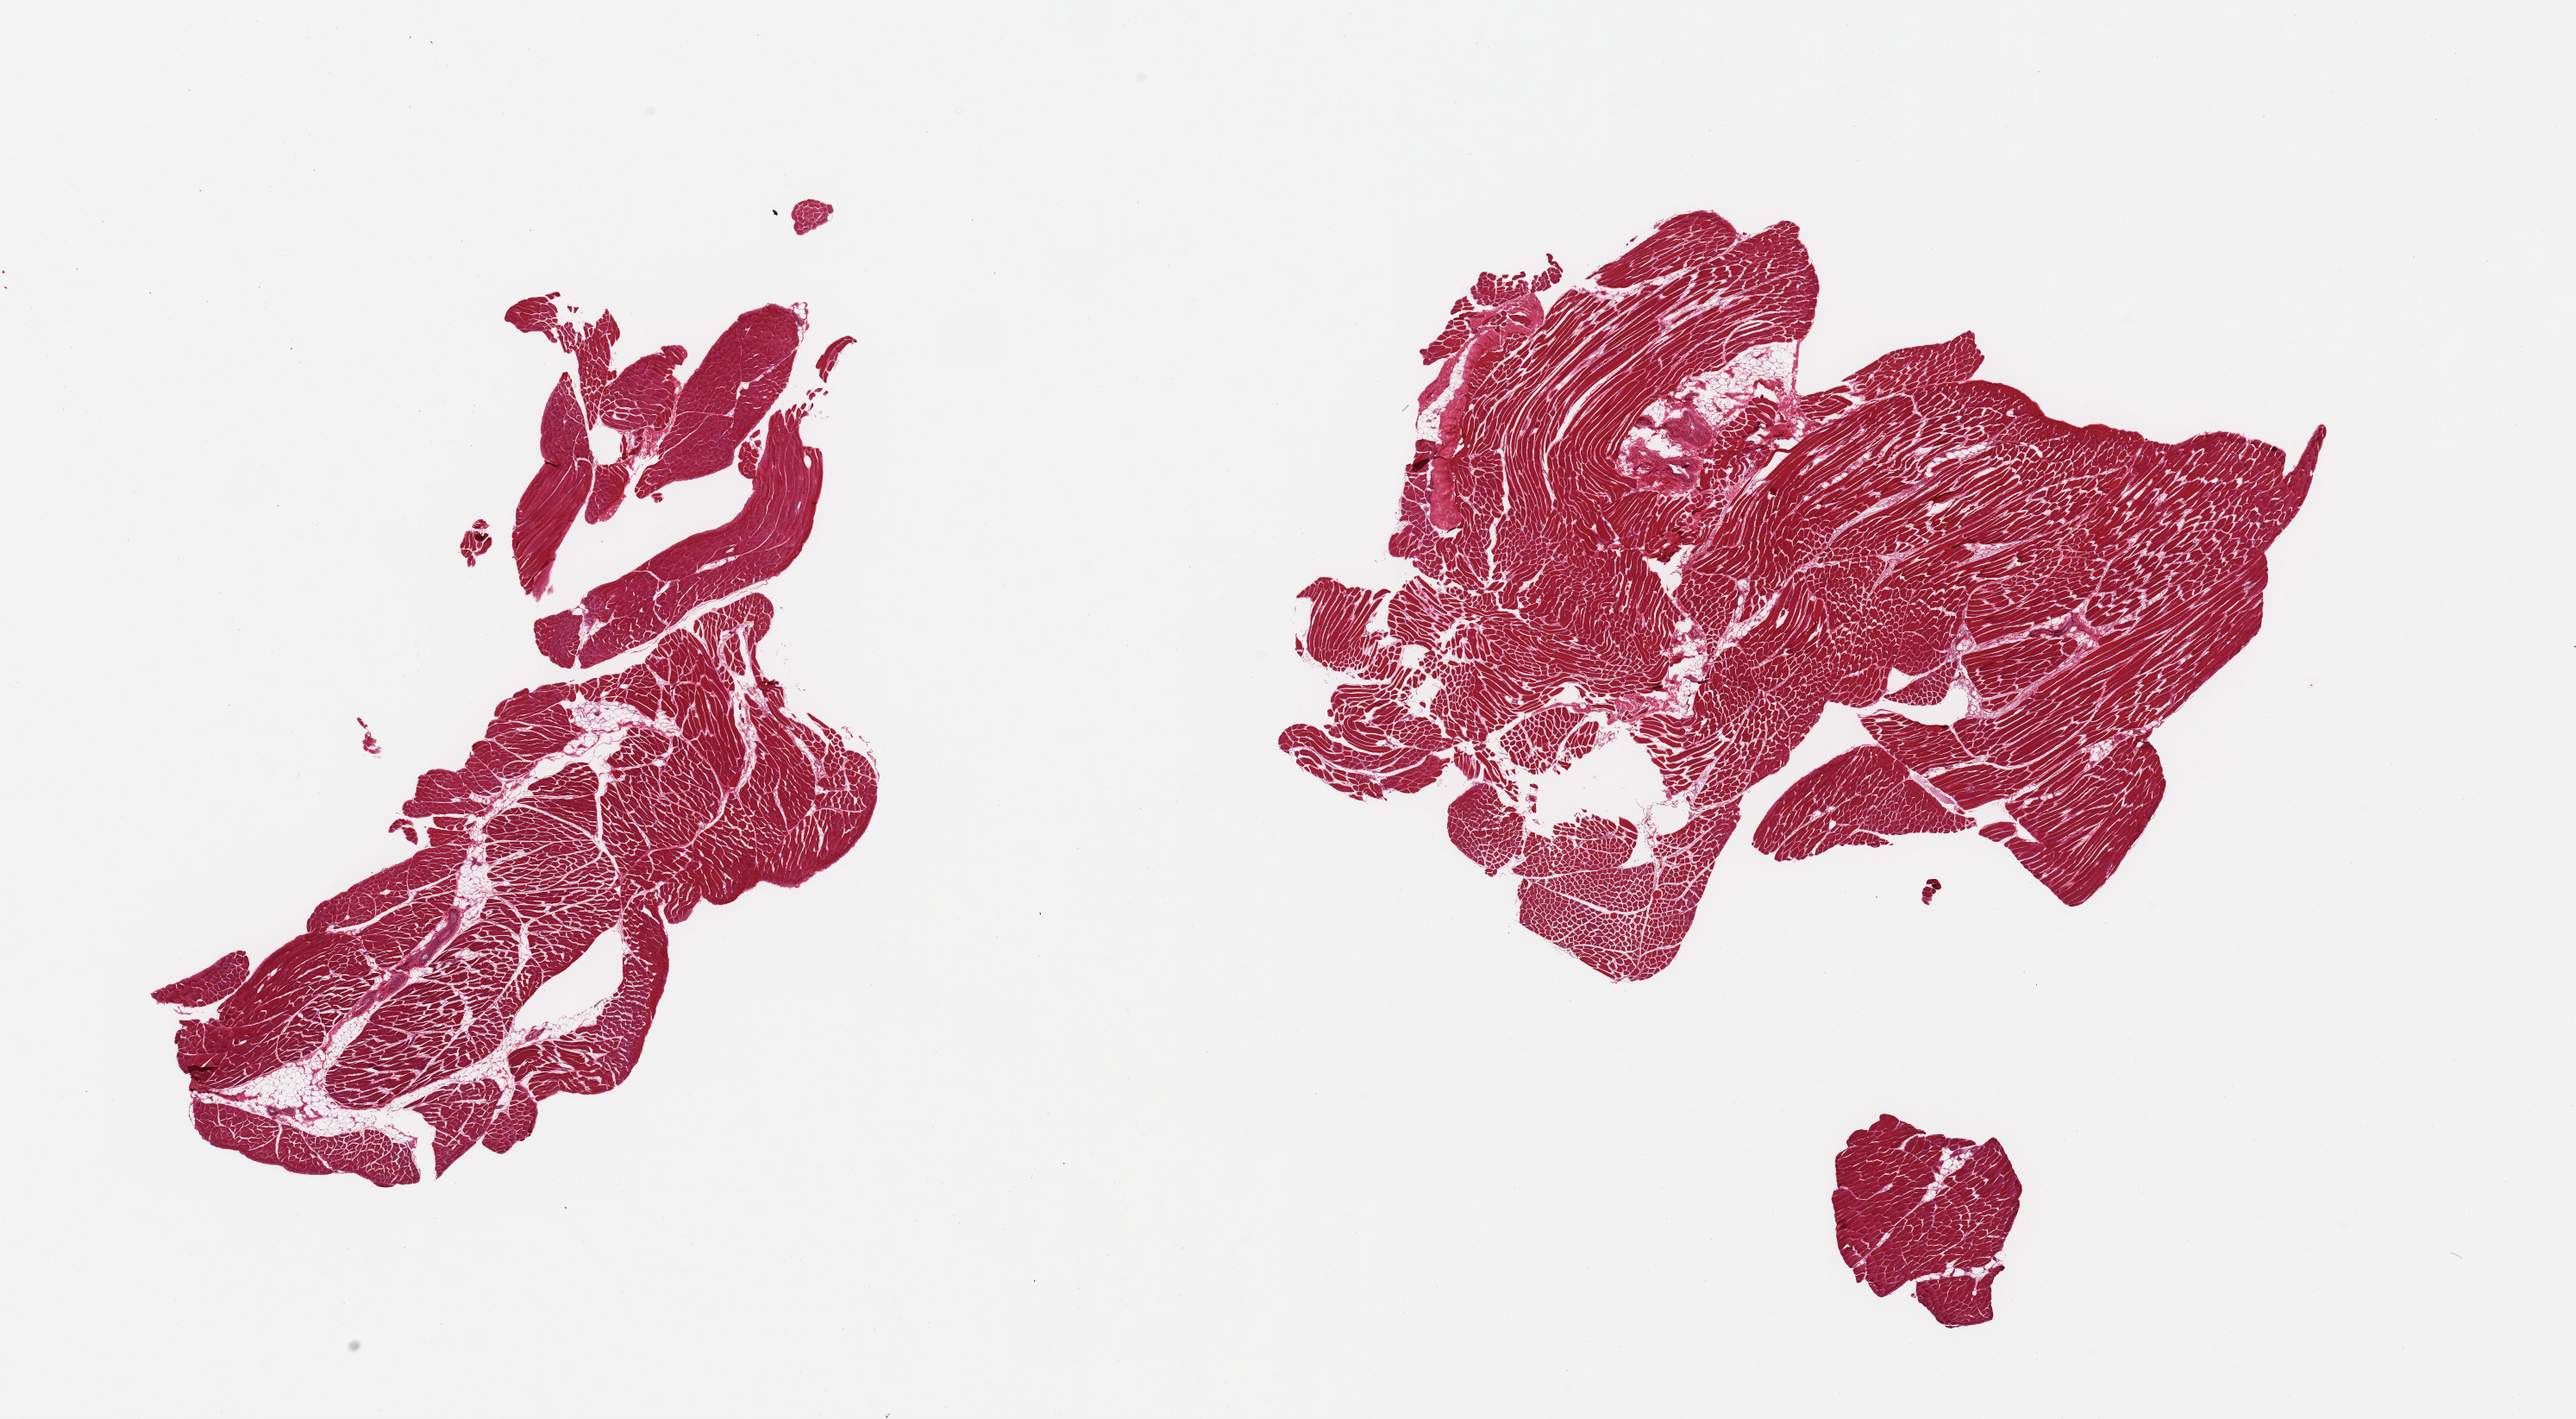
Digitized haematoxylin and eosin-stained section, a low-resolution overview of the entire scanned area, about 23.6 x 13.0 mm (from a 20x scan); PAXgene-fixed, paraffin-embedded tissue; sampled site (target tissue): skeletal muscle; tissue donor sample. Male donor.
Pathologist's review note for this sample: 2 fragmented pieces; 5% internal fat and vascular tissue.